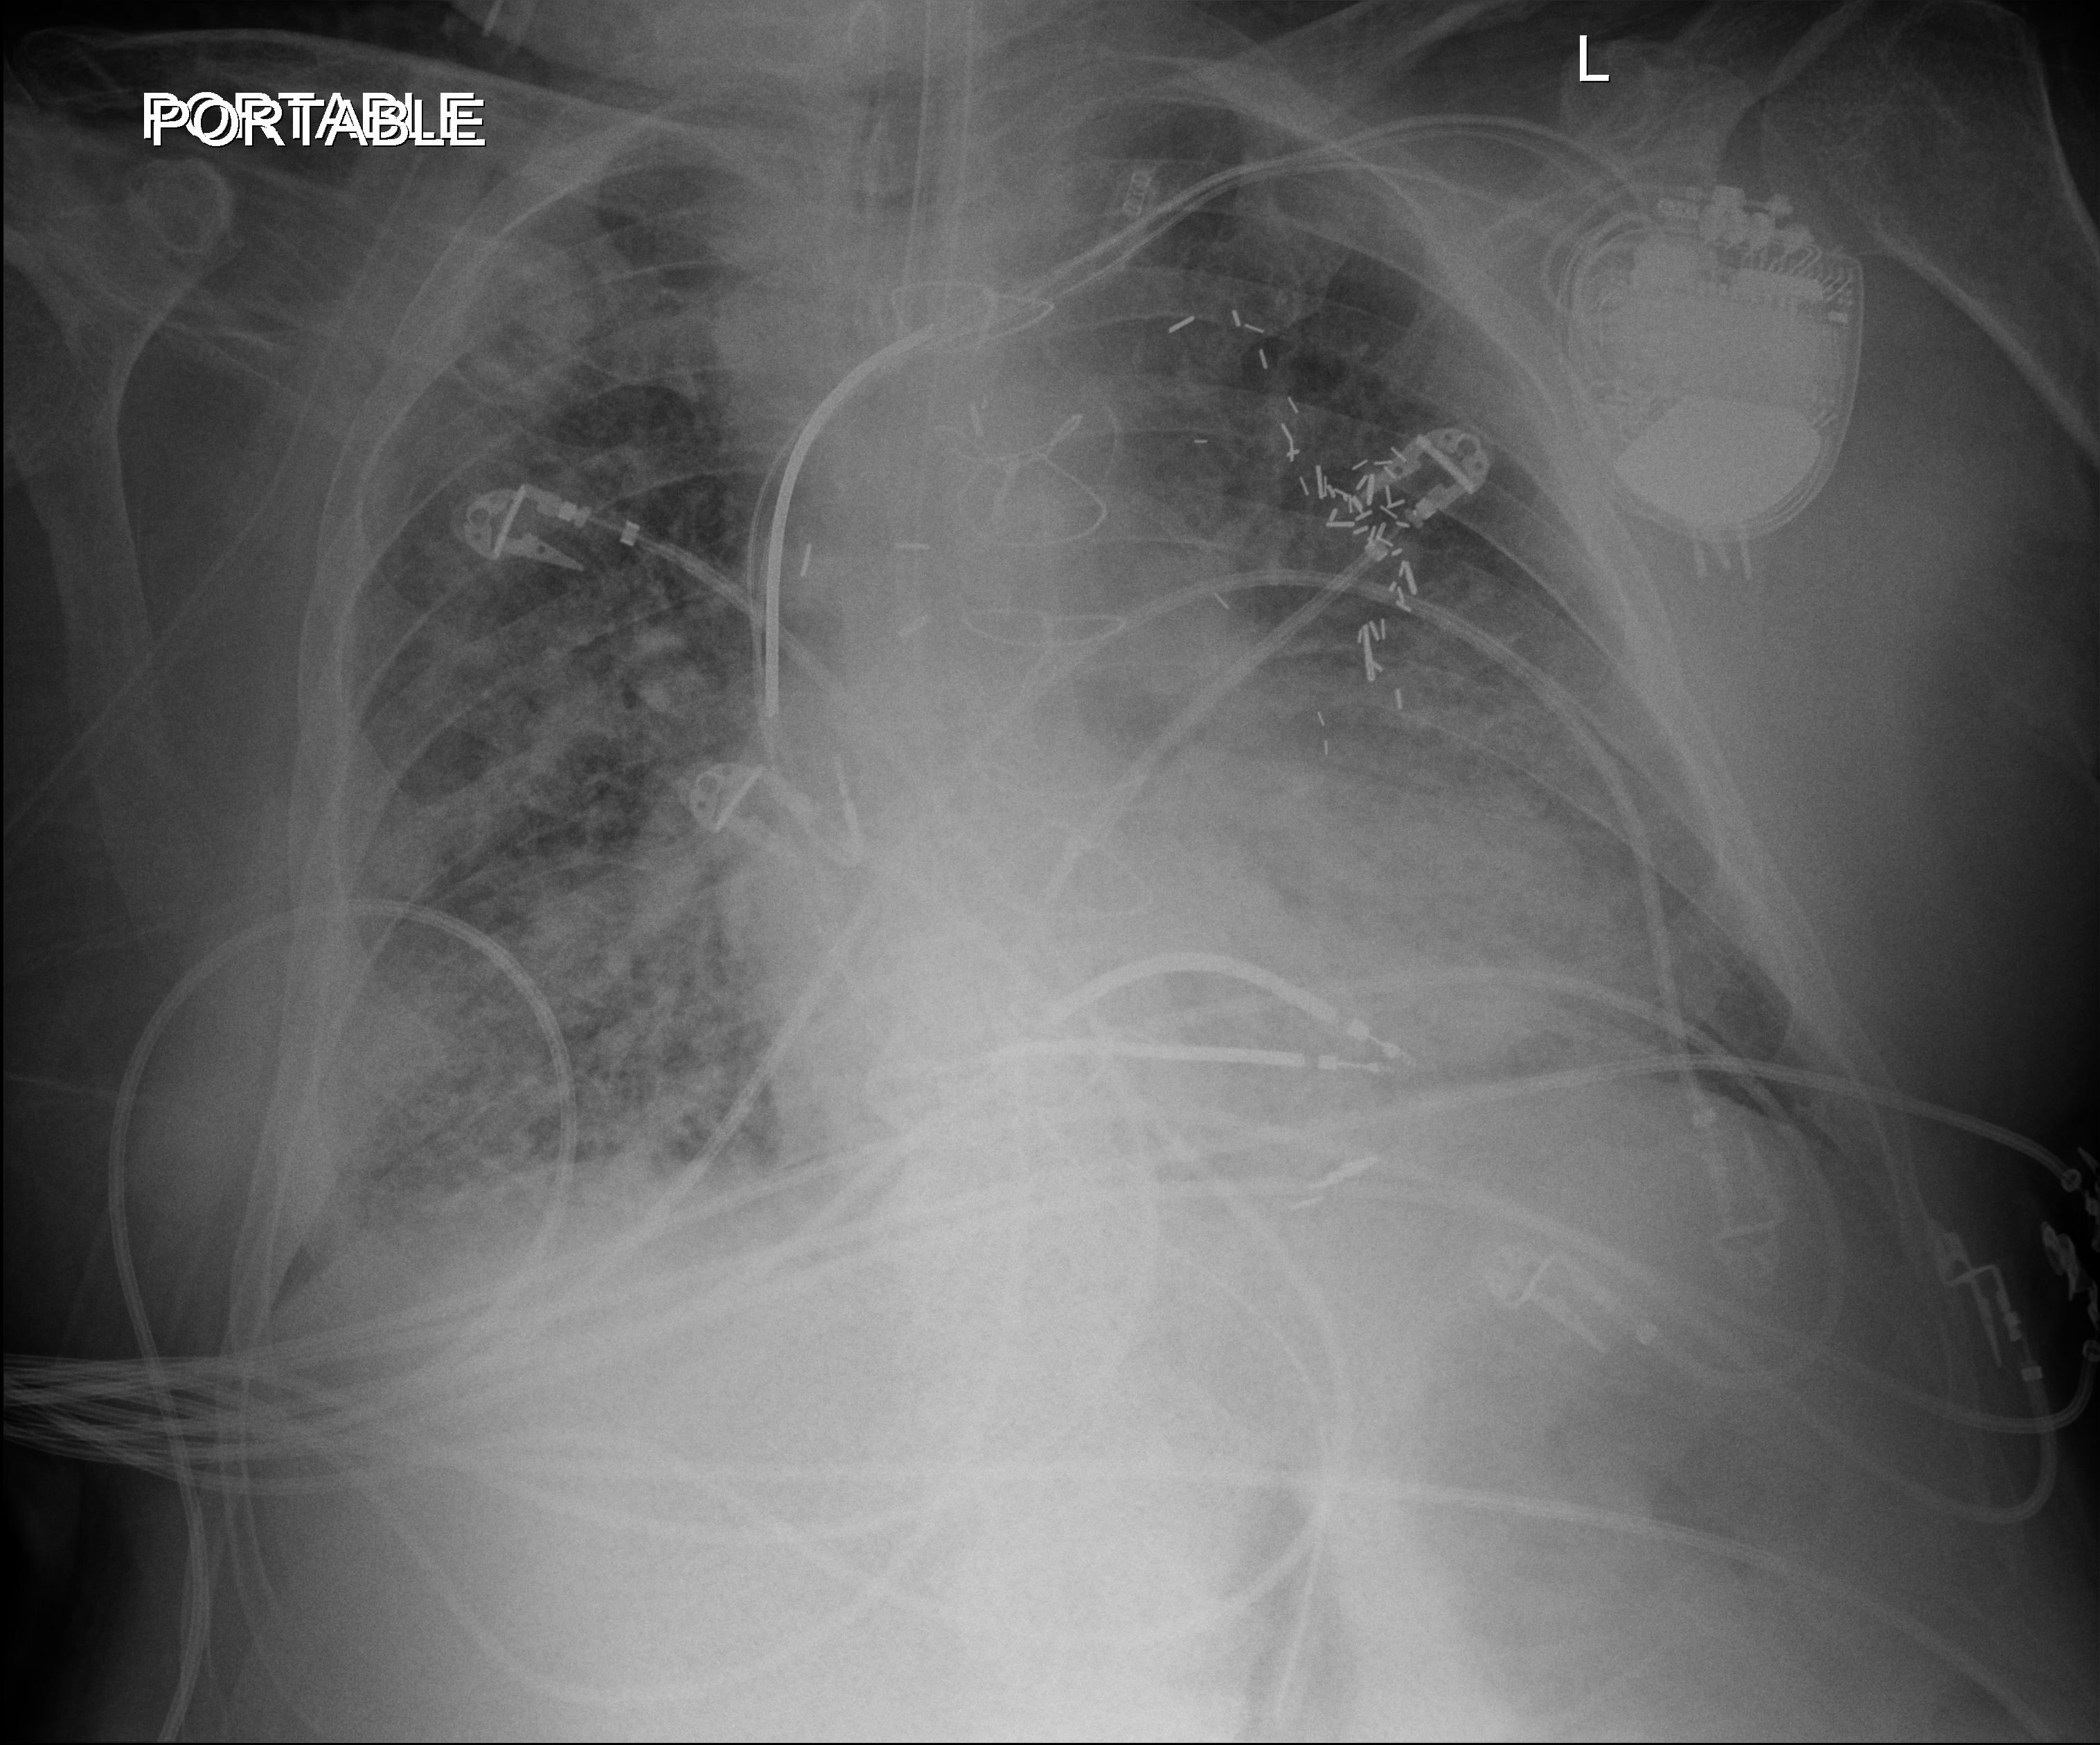
Chest X-ray (portable); anteroposterior (AP) projection. Male patient hospitalised with COVID-19, age 60–74 years.
Hospital-stay facts (about this admission, not read from this image; timing relative to this image not recorded): diabetes (admission record): yes; hypertension (admission record): yes.